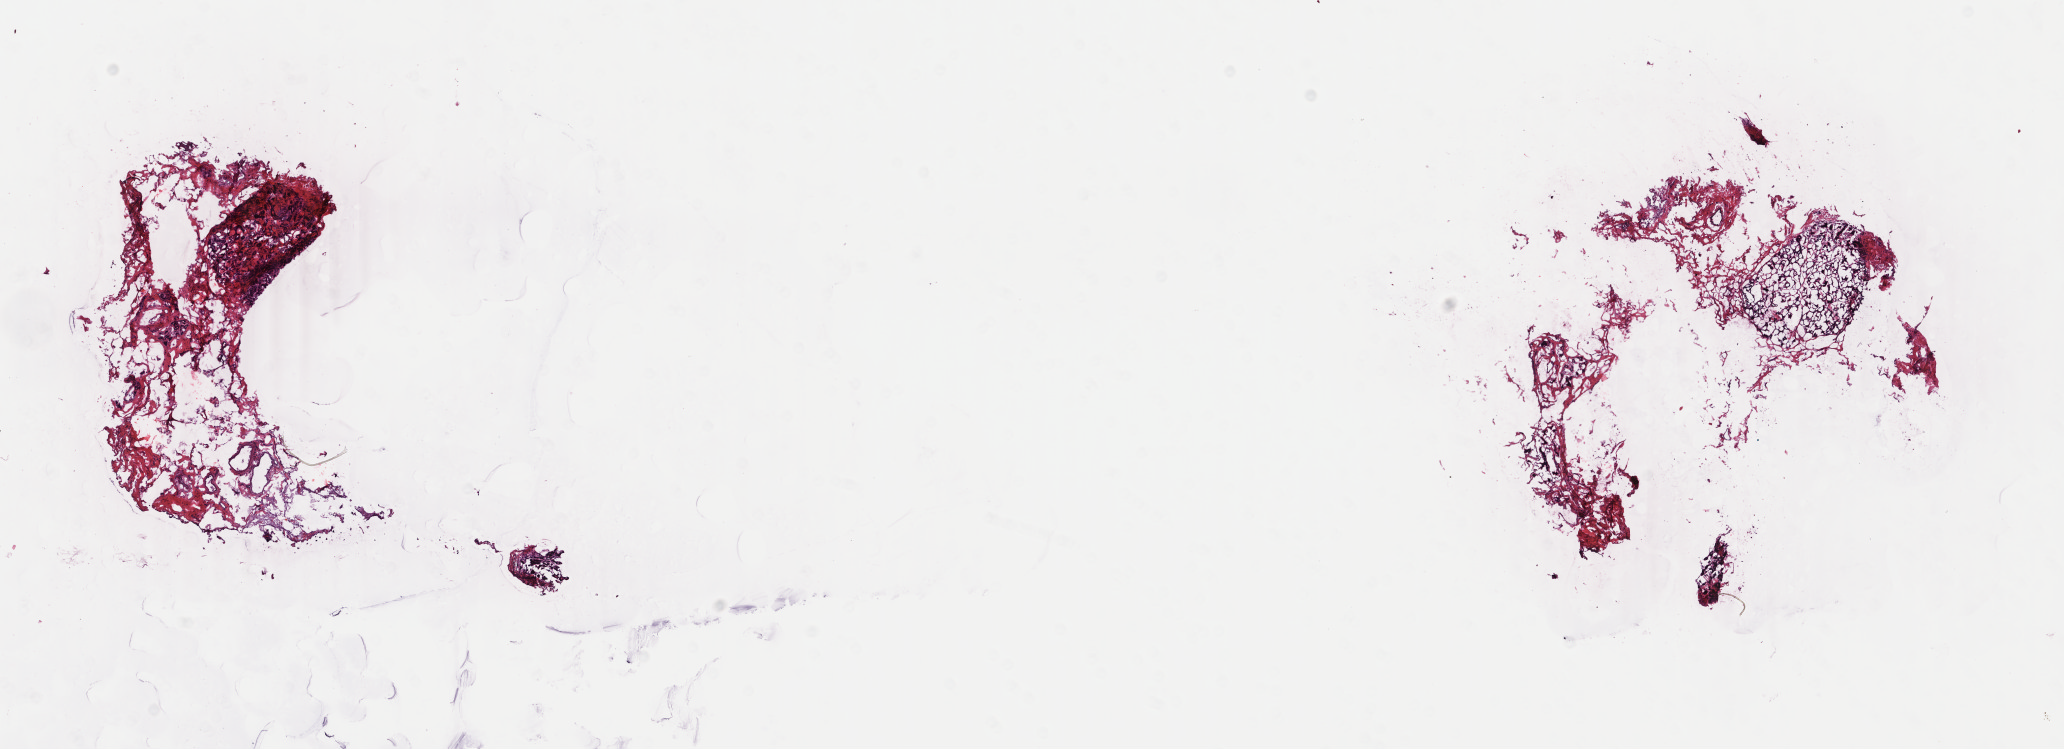
Whole-slide histology image, Hematoxylin and eosin (H&E) stained — whole scanned area (about 16.4 x 6.0 mm, acquisition: 40x scan) shown as a low-resolution overview; frozen section from the top of the tissue portion; sample: primary tumour, breast. Female, age 40 years at initial diagnosis. Slide review estimates, as recorded: tumour cells 50%, tumour nuclei 60%, normal cells 50%, stromal cells 0%, necrosis 0%. Infiltration values recorded for this section: lymphocyte infiltration 0%, monocyte infiltration 0%, neutrophil infiltration 0%.
AJCC pathologic stage: IA (3rd edition). Diagnosis: Infiltrating duct mixed with other types of carcinoma.